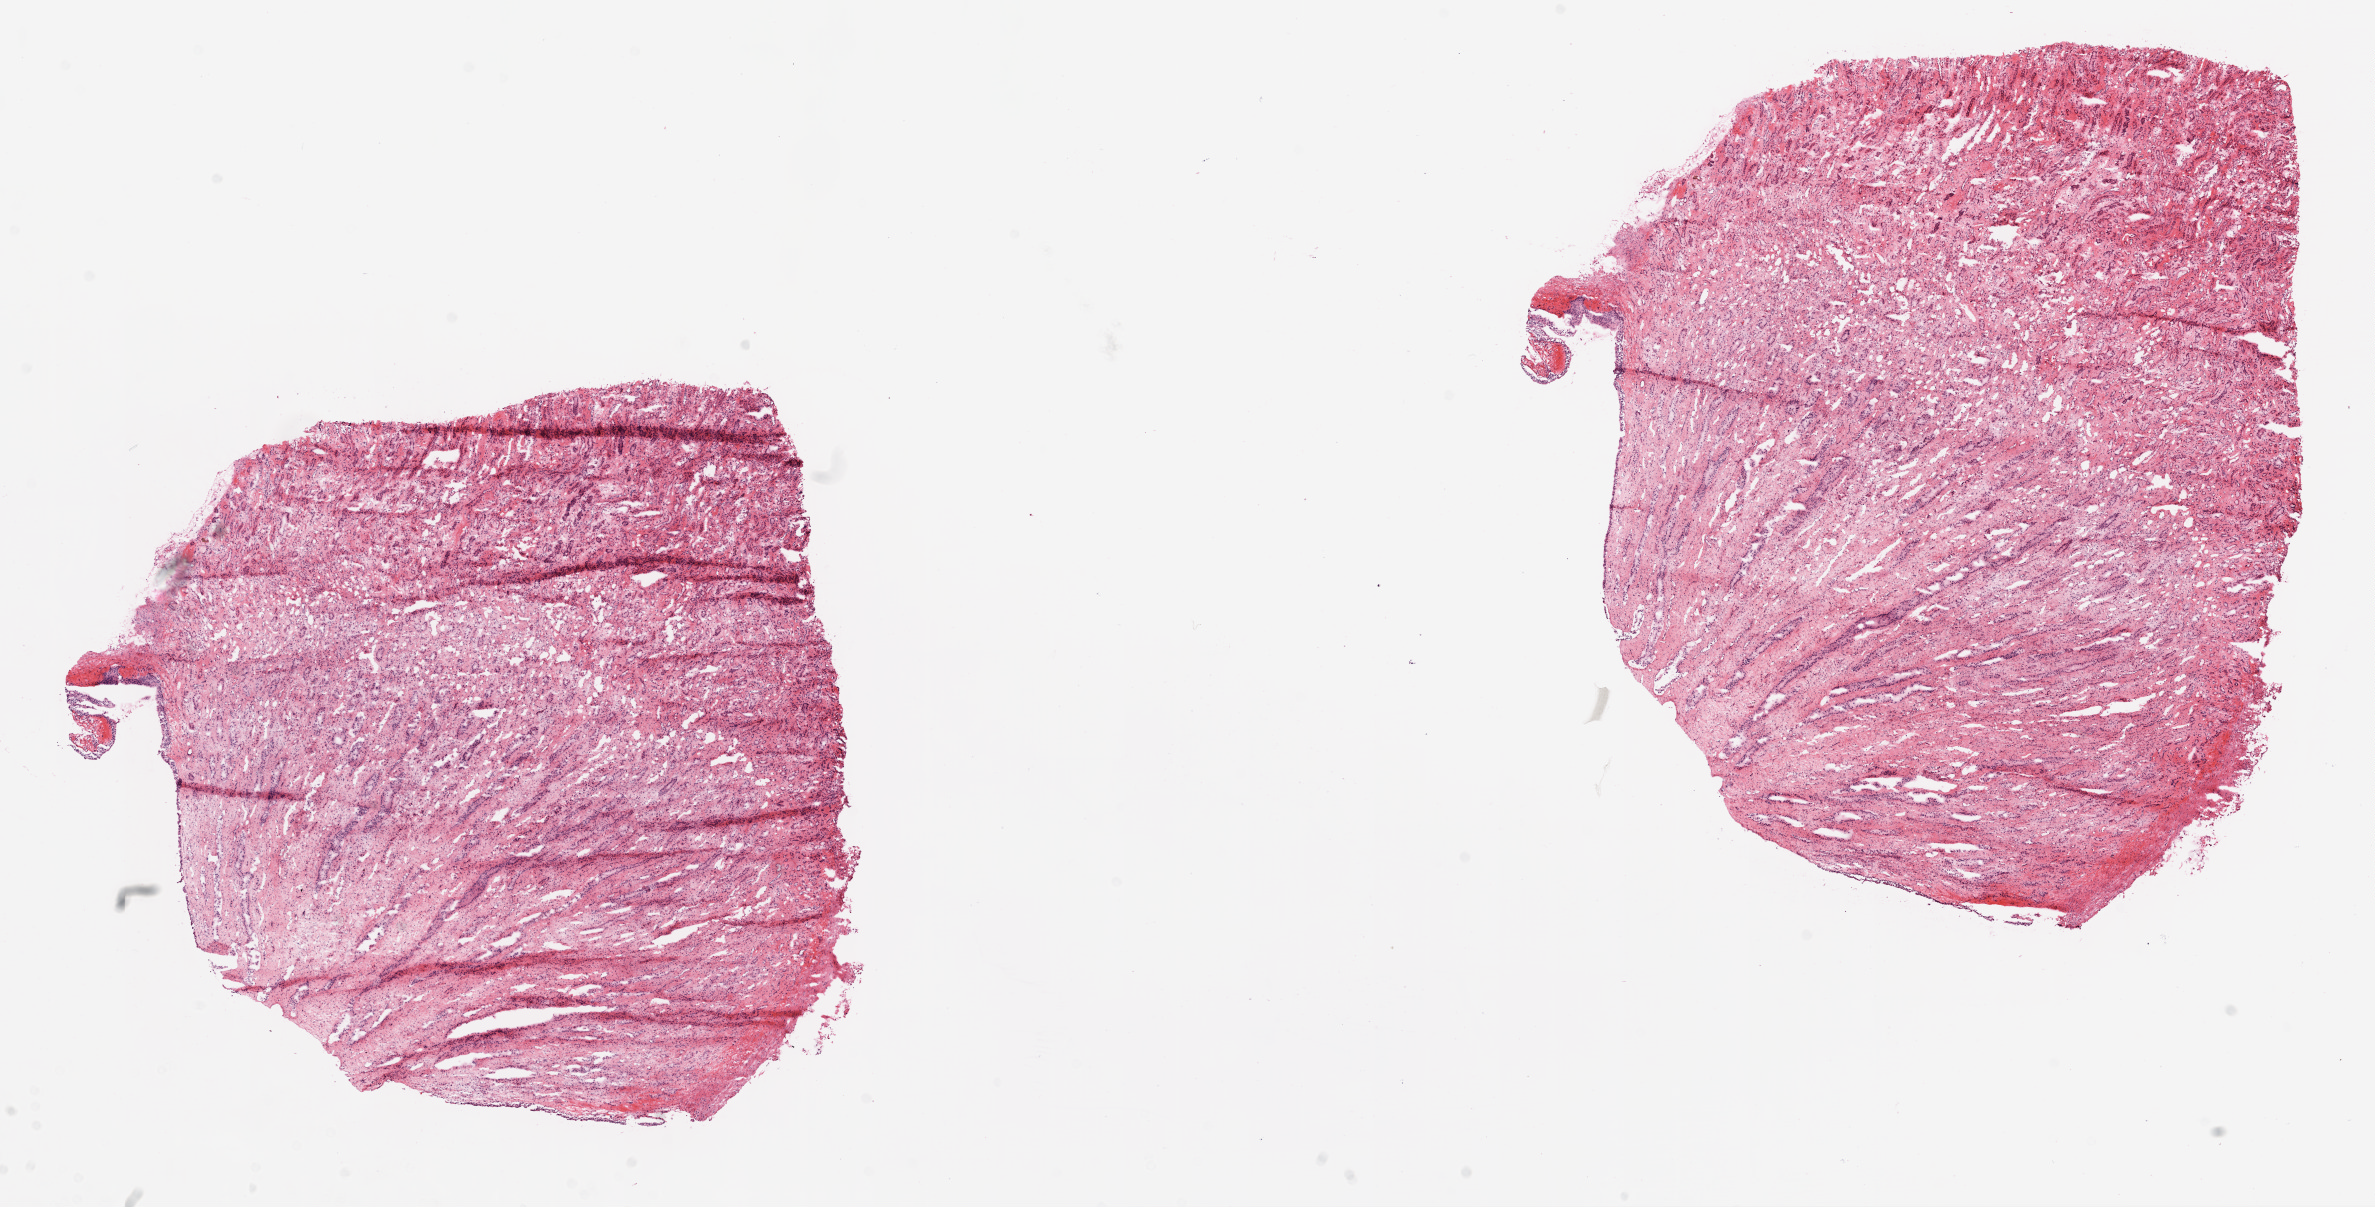
Whole-slide histology image, Hematoxylin and eosin (H&E) stained — low-resolution overview of the scanned area, about 19.1 x 9.7 mm (from a 20x scan), frozen section from the top of the tissue portion, kidney, solid tissue normal (non-tumour tissue) sample. Female patient; age at initial diagnosis 70 years.
This section: solid tissue normal sample (biorepository sample class). Patient diagnosis: Clear cell adenocarcinoma, NOS.